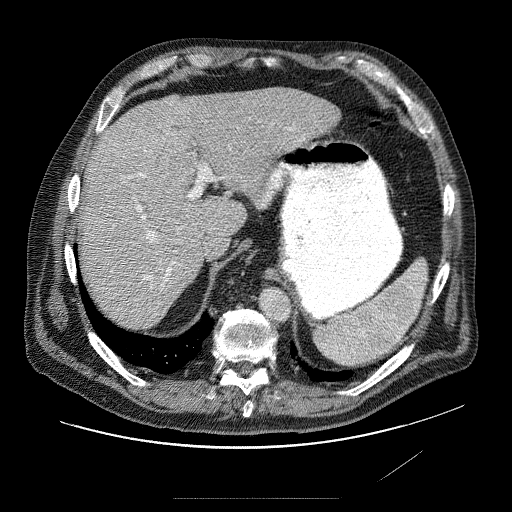
Contrast-enhanced abdominal CT (liver protocol), one axial slice; reconstruction kernel STANDARD; 120 kVp; soft-tissue window (W 400 / L 40 HU); 2.5 mm slice thickness; 512 × 512 image matrix. Case-level facts recorded for this patient, not image findings: diagnosis: hepatocellular carcinoma (patient treated with transarterial chemoembolisation; whether this scan precedes or follows treatment is not stated here); TNM stage (as recorded): Stage-IVA; Child-Pugh class: A; tumour differentiation: moderately differentiated; tumour nodularity: multinodular.
Outlined on this slice (semi-automatically segmented with operator editing):
- abdominal aorta: bounding box [x1, y1, x2, y2] px = [259, 289, 291, 319]
- liver parenchyma outside the tumour (the mass and vessels are separate outlines, so this box may not span the whole liver): [82, 86, 344, 314]
- mass: [96, 102, 272, 290]
- liver vessels: [130, 108, 296, 287]